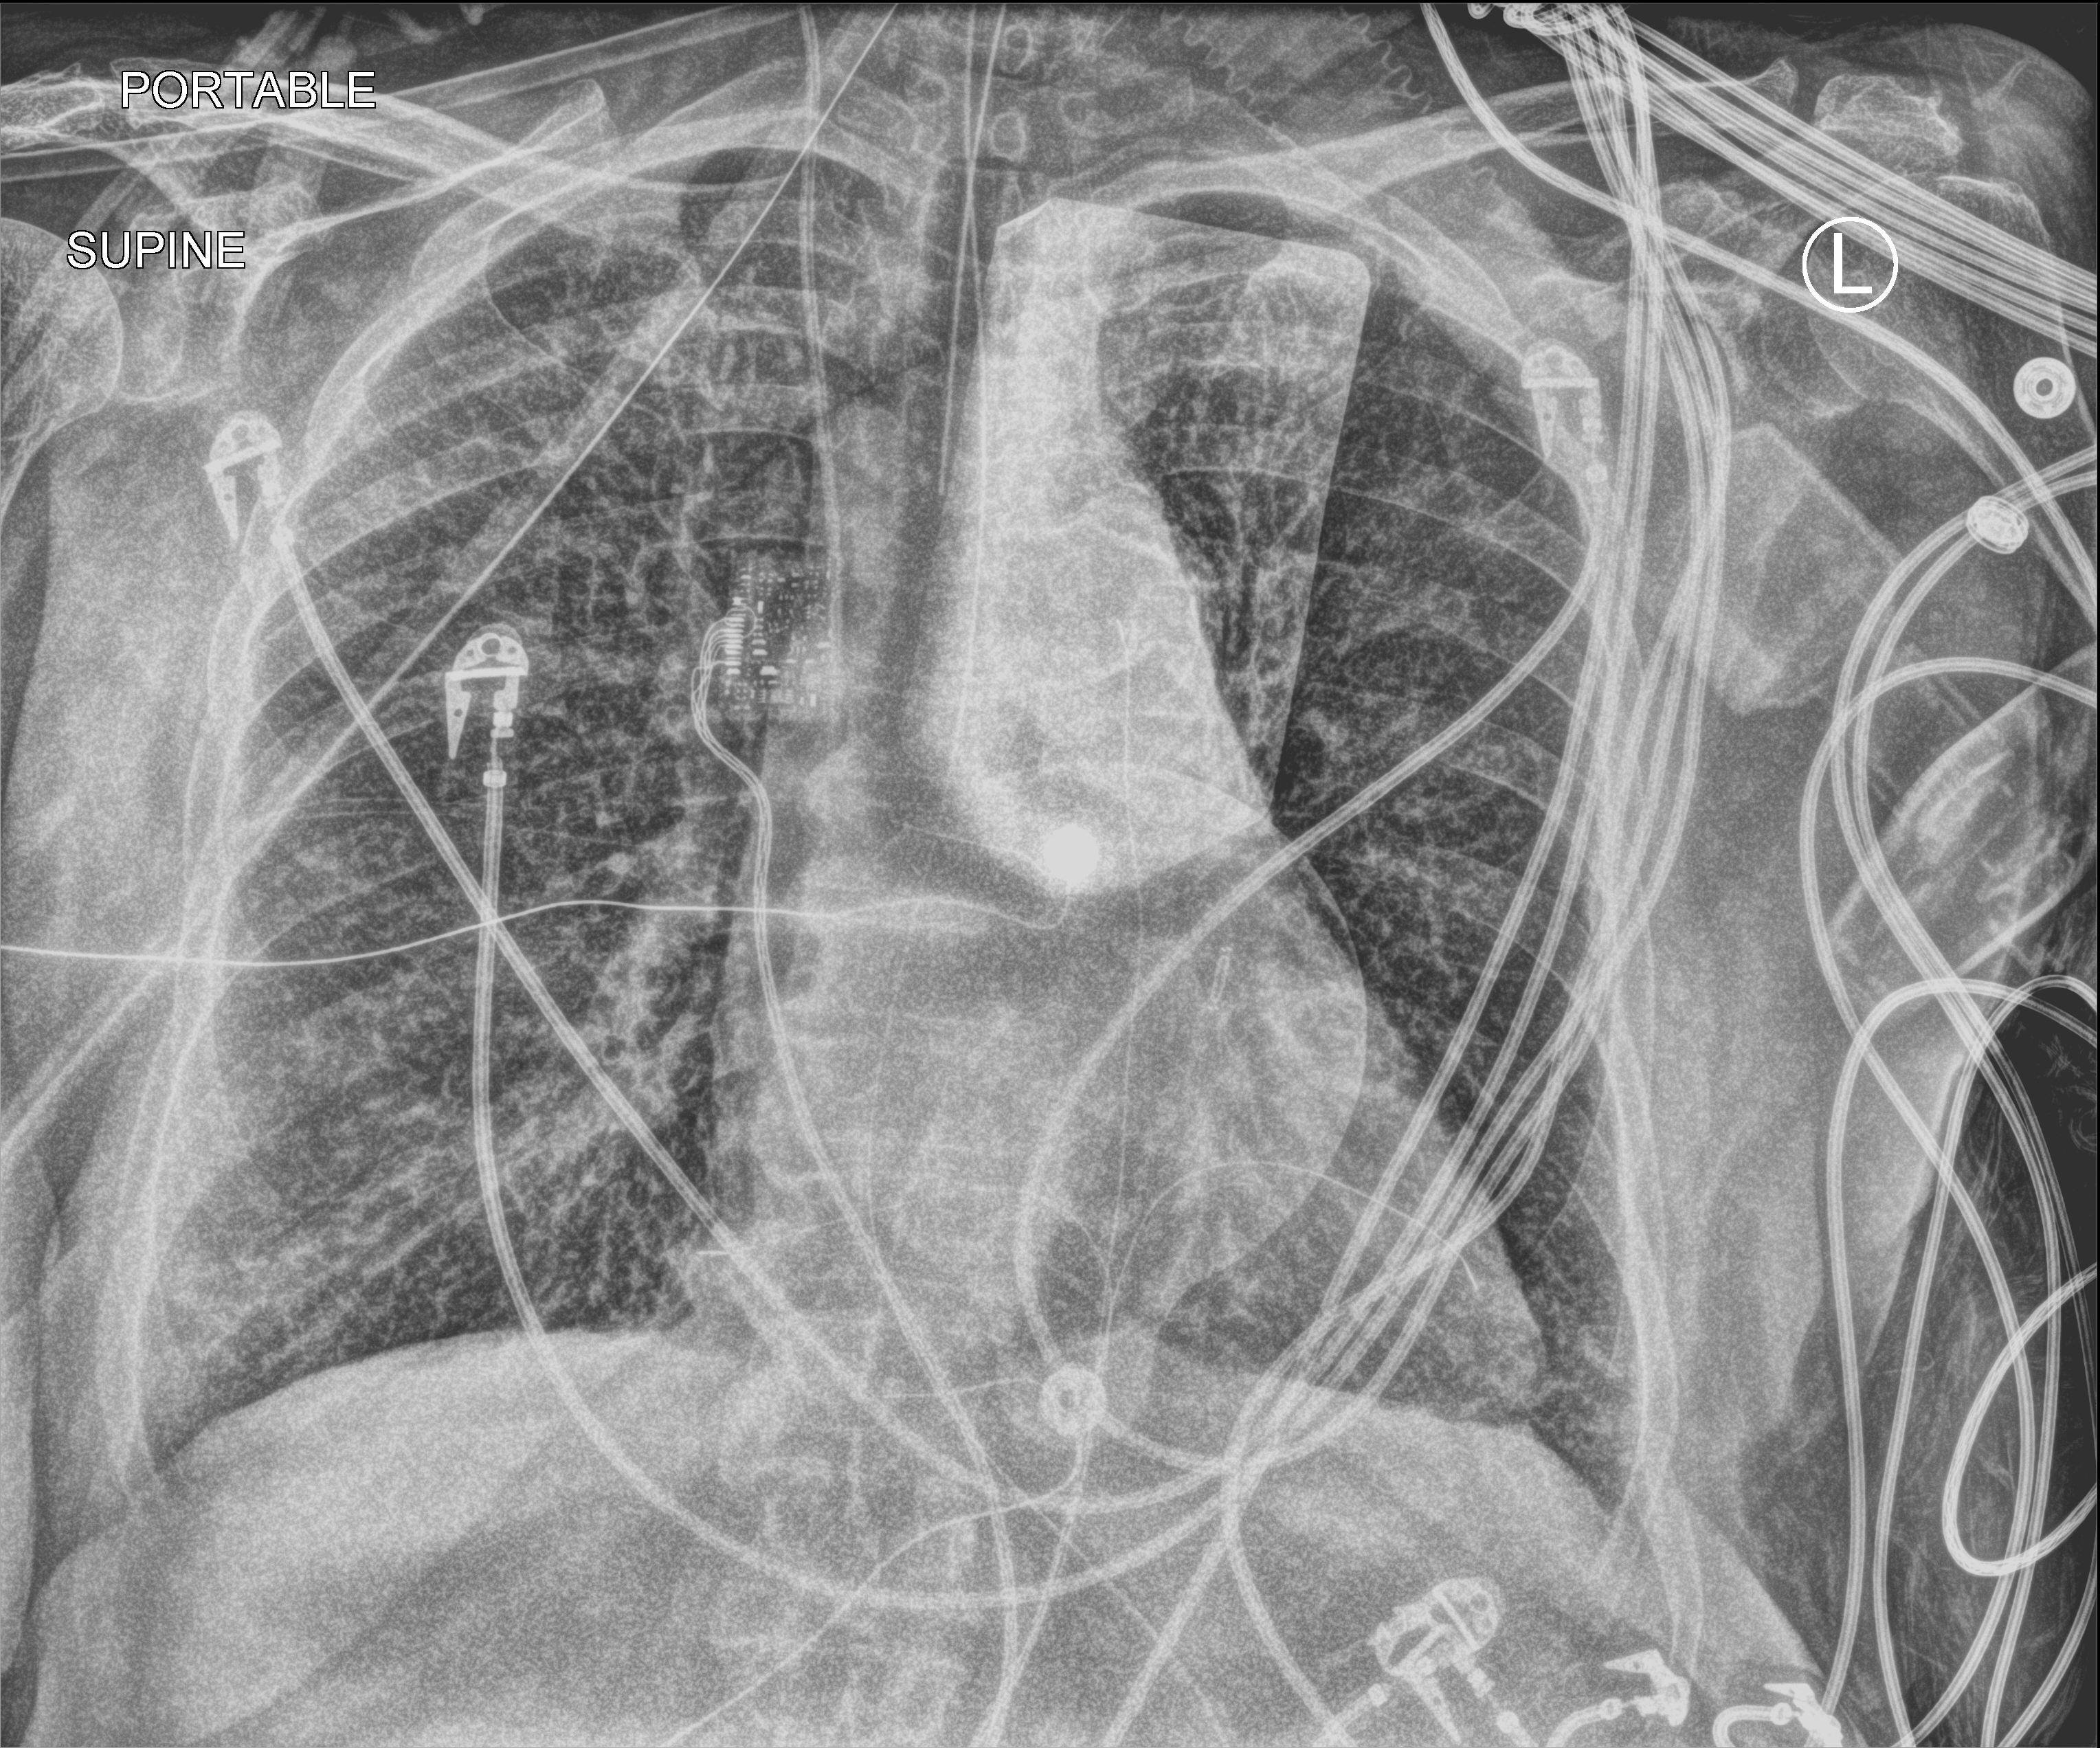
Chest X-ray (portable). Female patient hospitalised with COVID-19, age 75–90 years.
Hospital-stay facts (about this admission, not read from this image; timing relative to this image not recorded): mechanically ventilated during this hospital stay: yes; length of hospital stay: 10 days; admitted to intensive care during this hospital stay: yes.